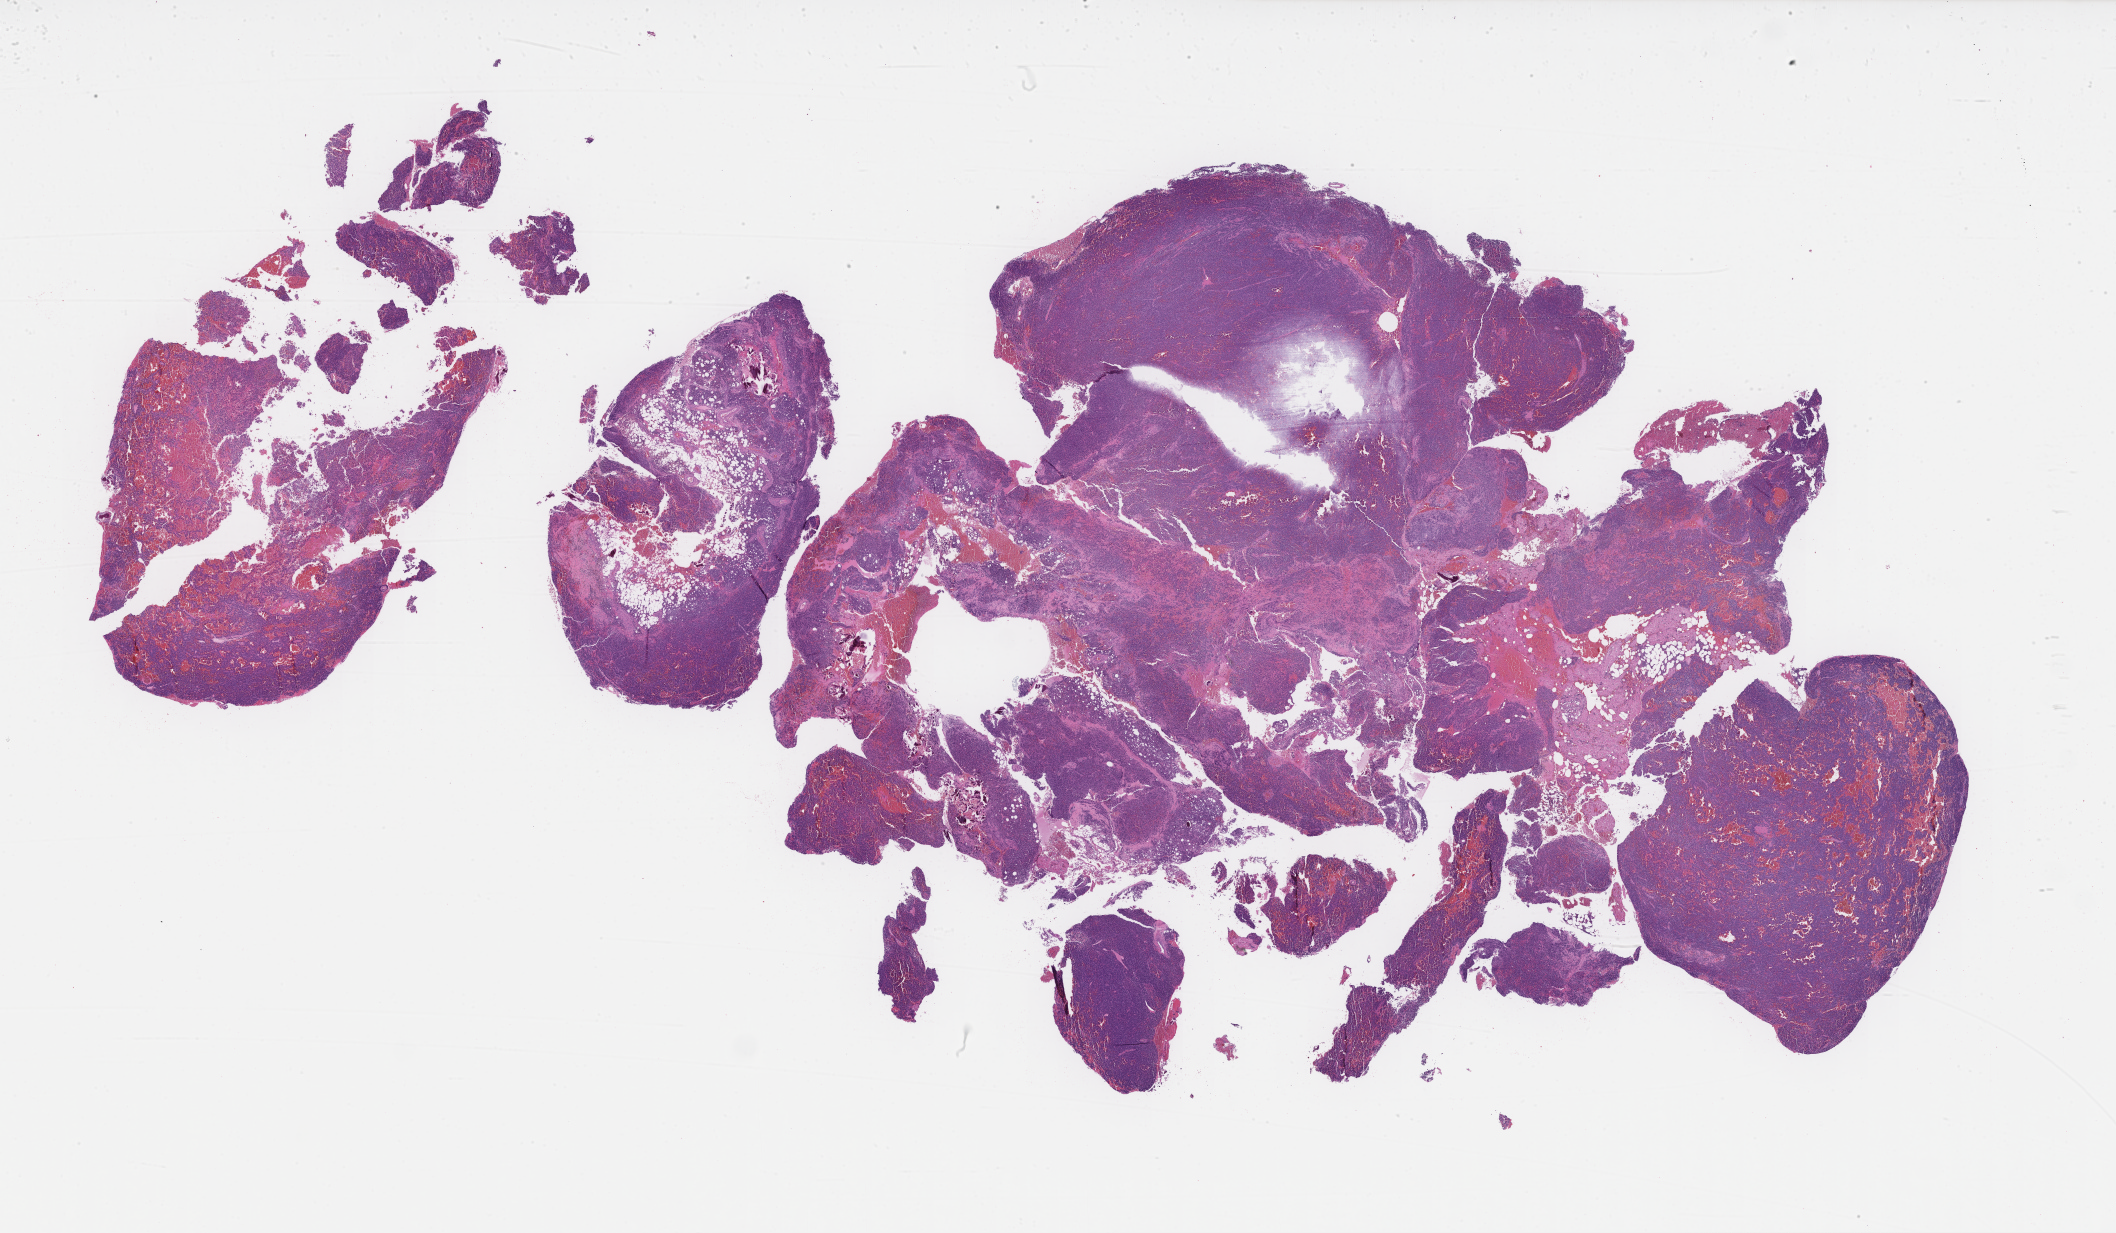
Digitized H&E-stained section, shown as a low-resolution overview of the whole scanned area (about 34.2 x 19.9 mm). Formalin-fixed paraffin-embedded section. Archival tissue. Patient: female.
This section: metastatic tumor tissue. Primary diagnosis of the patient: Plasma Cell Myeloma.